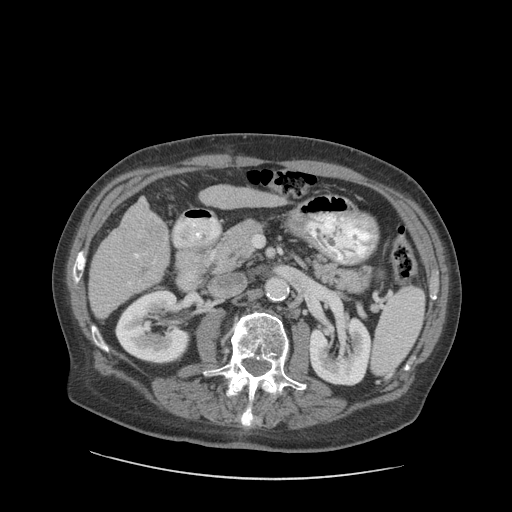
Contrast-enhanced abdominal CT (liver protocol), one axial slice; slice 37 of 89 in the series (ordered by position); reconstruction kernel STANDARD; 140 kVp; soft-tissue window (W 400 / L 40 HU); 2.5 mm slice thickness; 512 × 512 image matrix. Case-level facts recorded for this patient, not image findings: diagnosis: hepatocellular carcinoma (patient treated with transarterial chemoembolisation; whether this scan precedes or follows treatment is not stated here); TNM stage (as recorded): Stage-I.
Annotated regions visible in this slice (semi-automatic segmentation, software-assisted and operator-edited):
- liver parenchyma outside the tumour (the mass and vessels are separate outlines, so this box may not span the whole liver): bounding box <88,198,170,318> (left, top, right, bottom; pixels)
- mass: <125,210,168,280>
- liver vessels: <114,235,156,286>